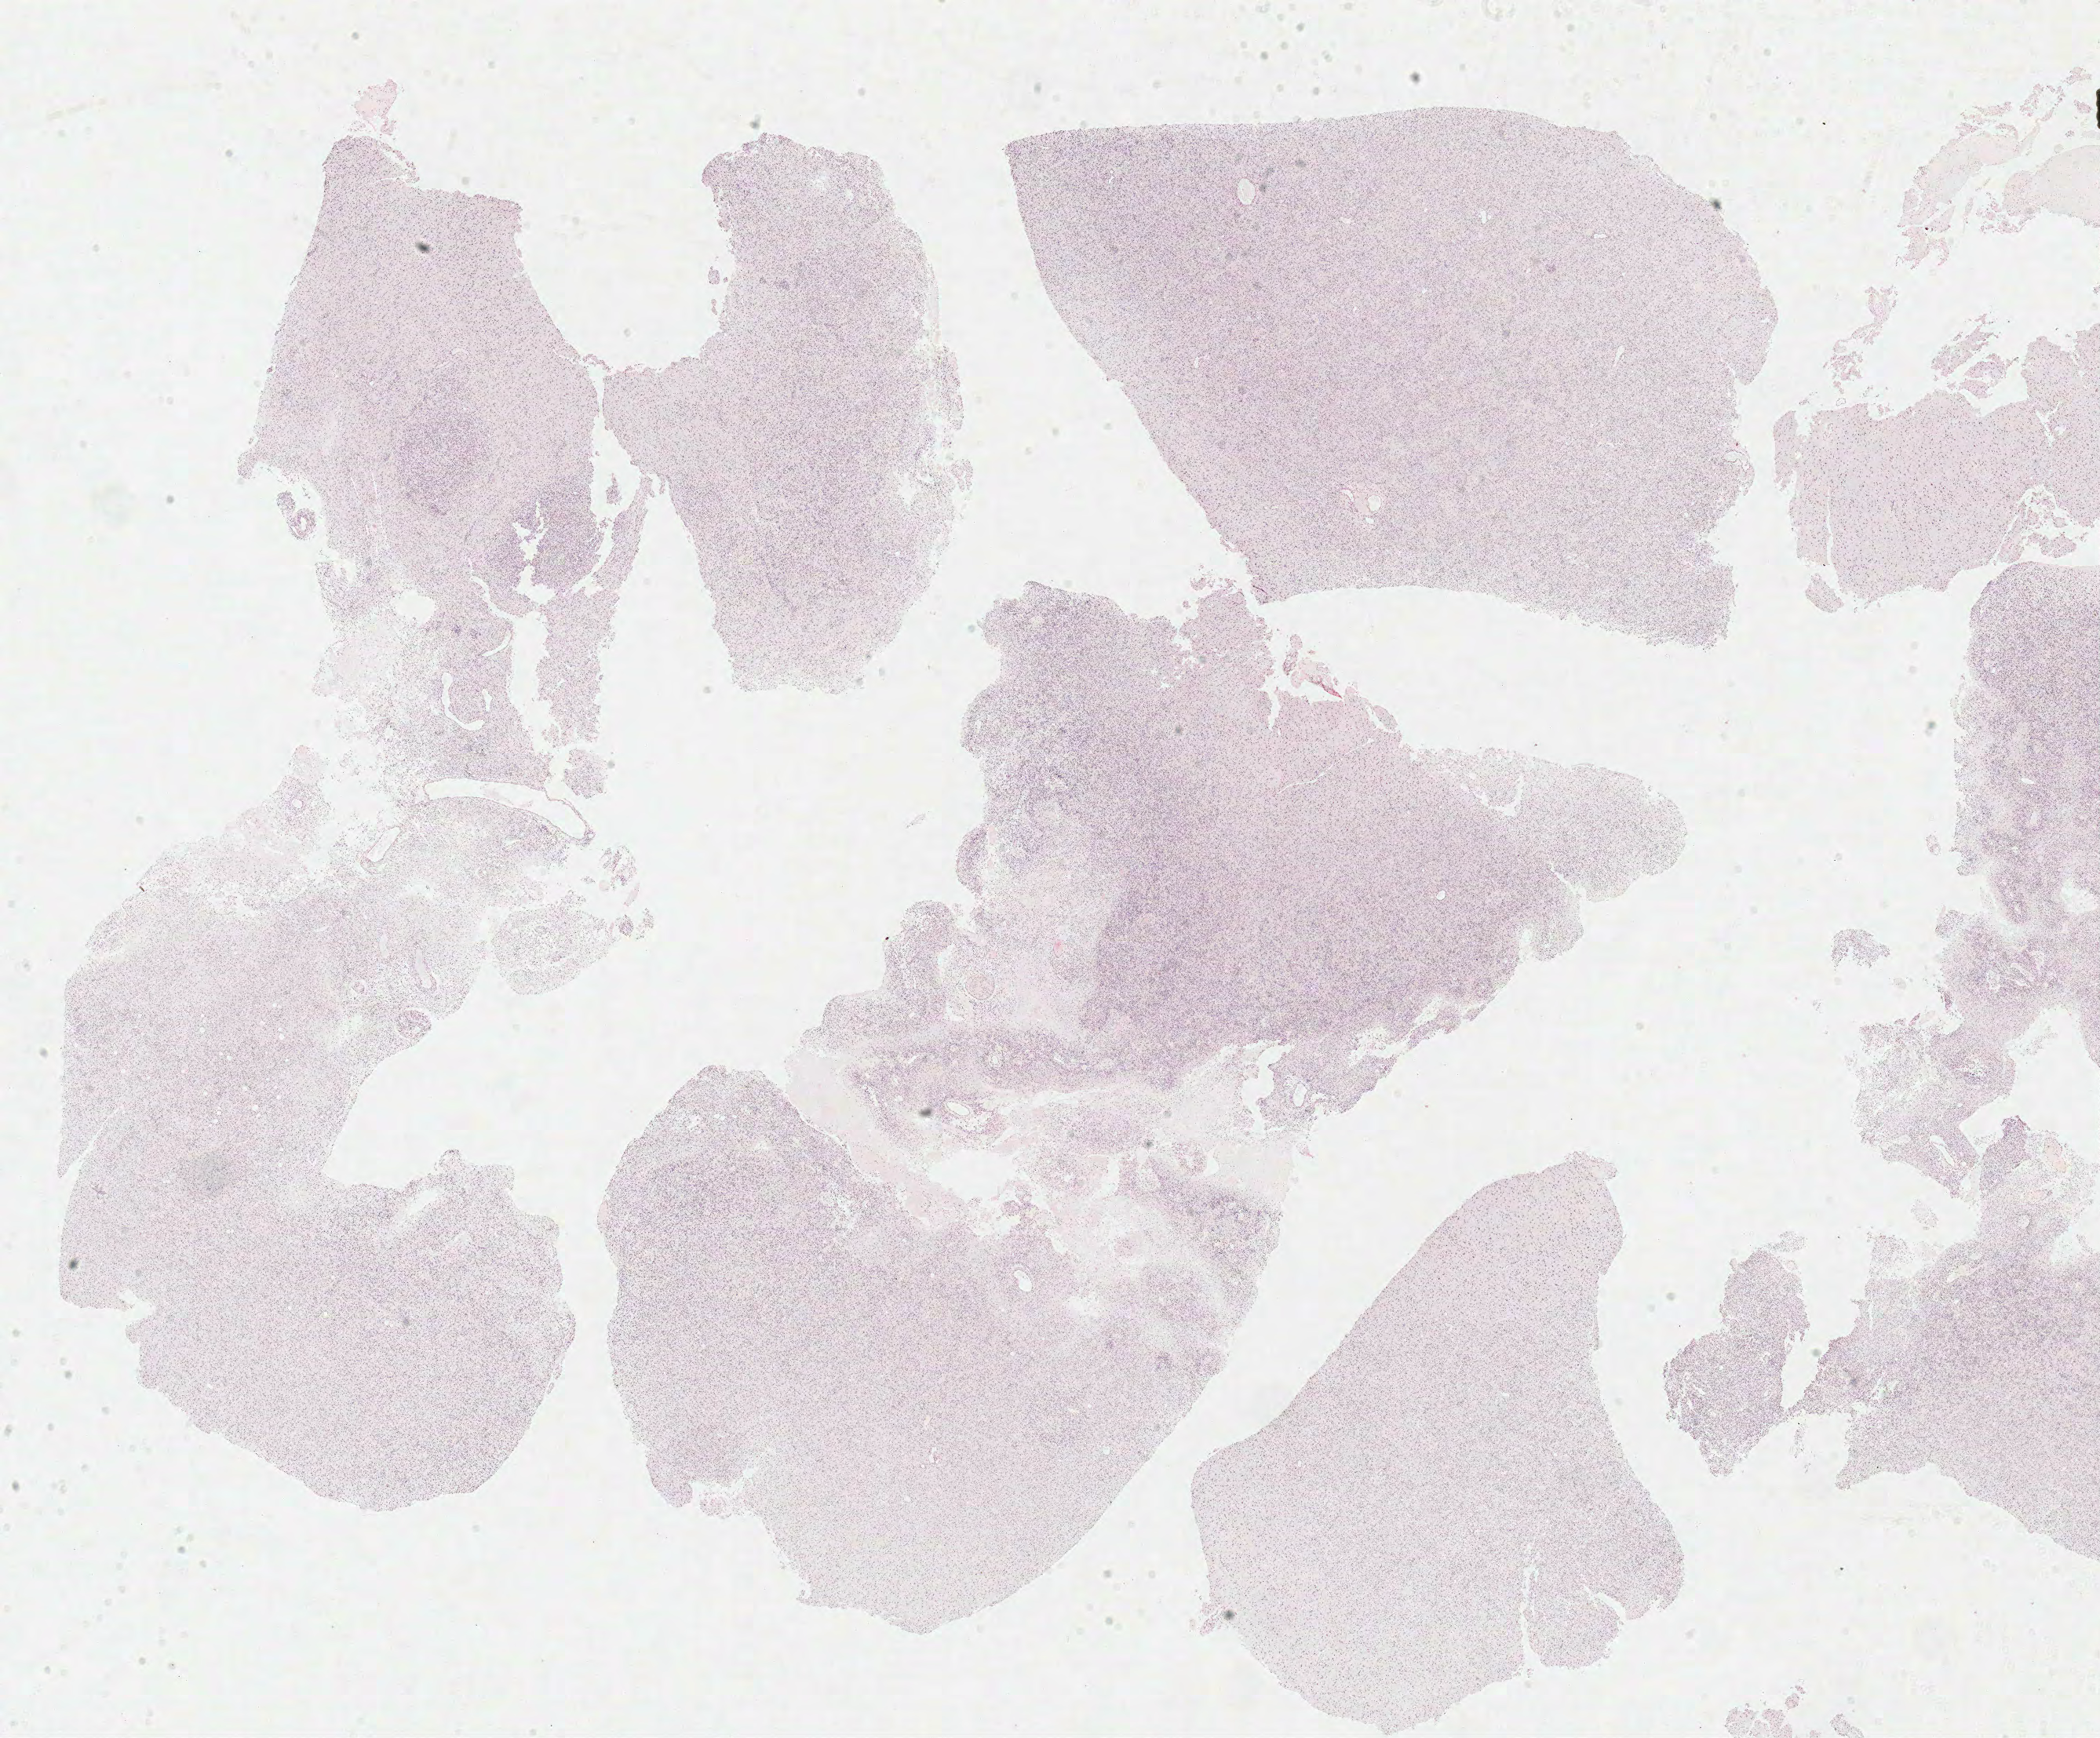
Whole-slide histology image, H&E-stained — whole scanned area (about 21.0 x 17.4 mm, from a 40x scan) shown as a low-resolution overview. Formalin-fixed paraffin-embedded (FFPE) diagnostic section. Primary tumour sample from the brain. Male, age 81 years at initial diagnosis.
Pathologic diagnosis: Glioblastoma.